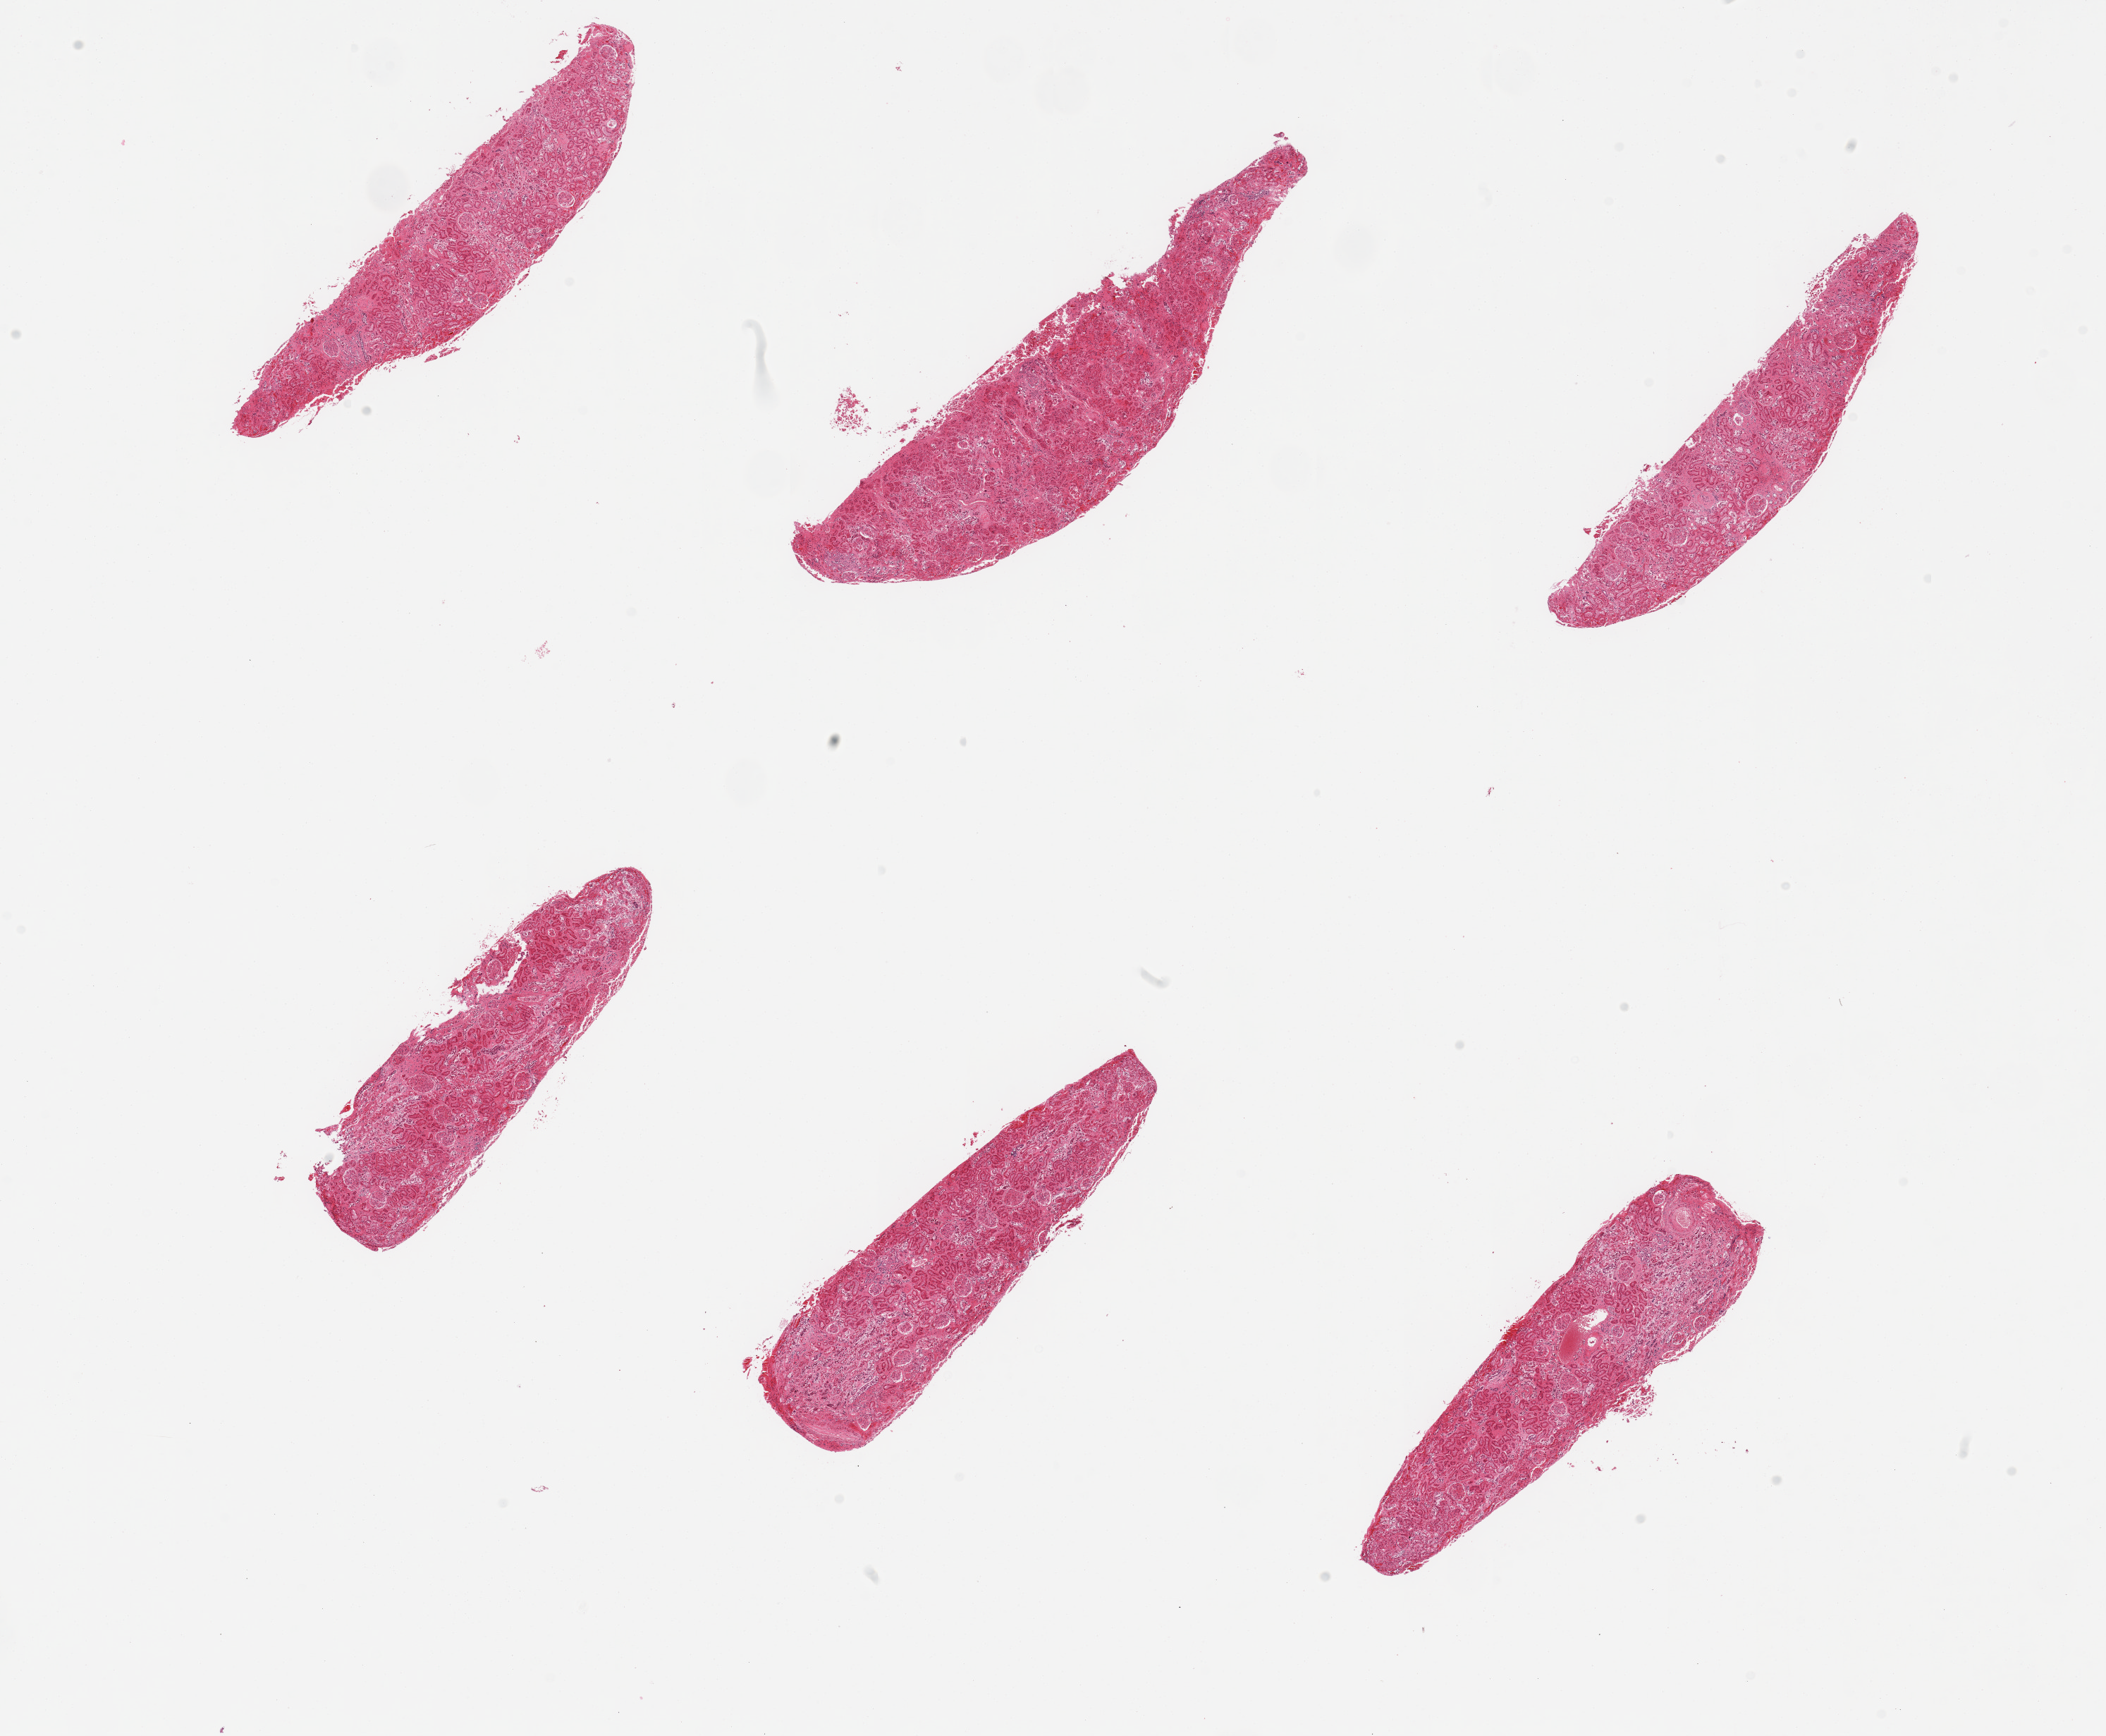
H&E whole-slide image — shown as a low-resolution overview of the whole scanned area (about 23.6 x 19.5 mm); PAXgene-fixed, paraffin-embedded tissue; target tissue: renal cortex; donor tissue sample. Male donor.
Pathologist's review note for this sample: 6 pieces; arterial nephrosclerosis.